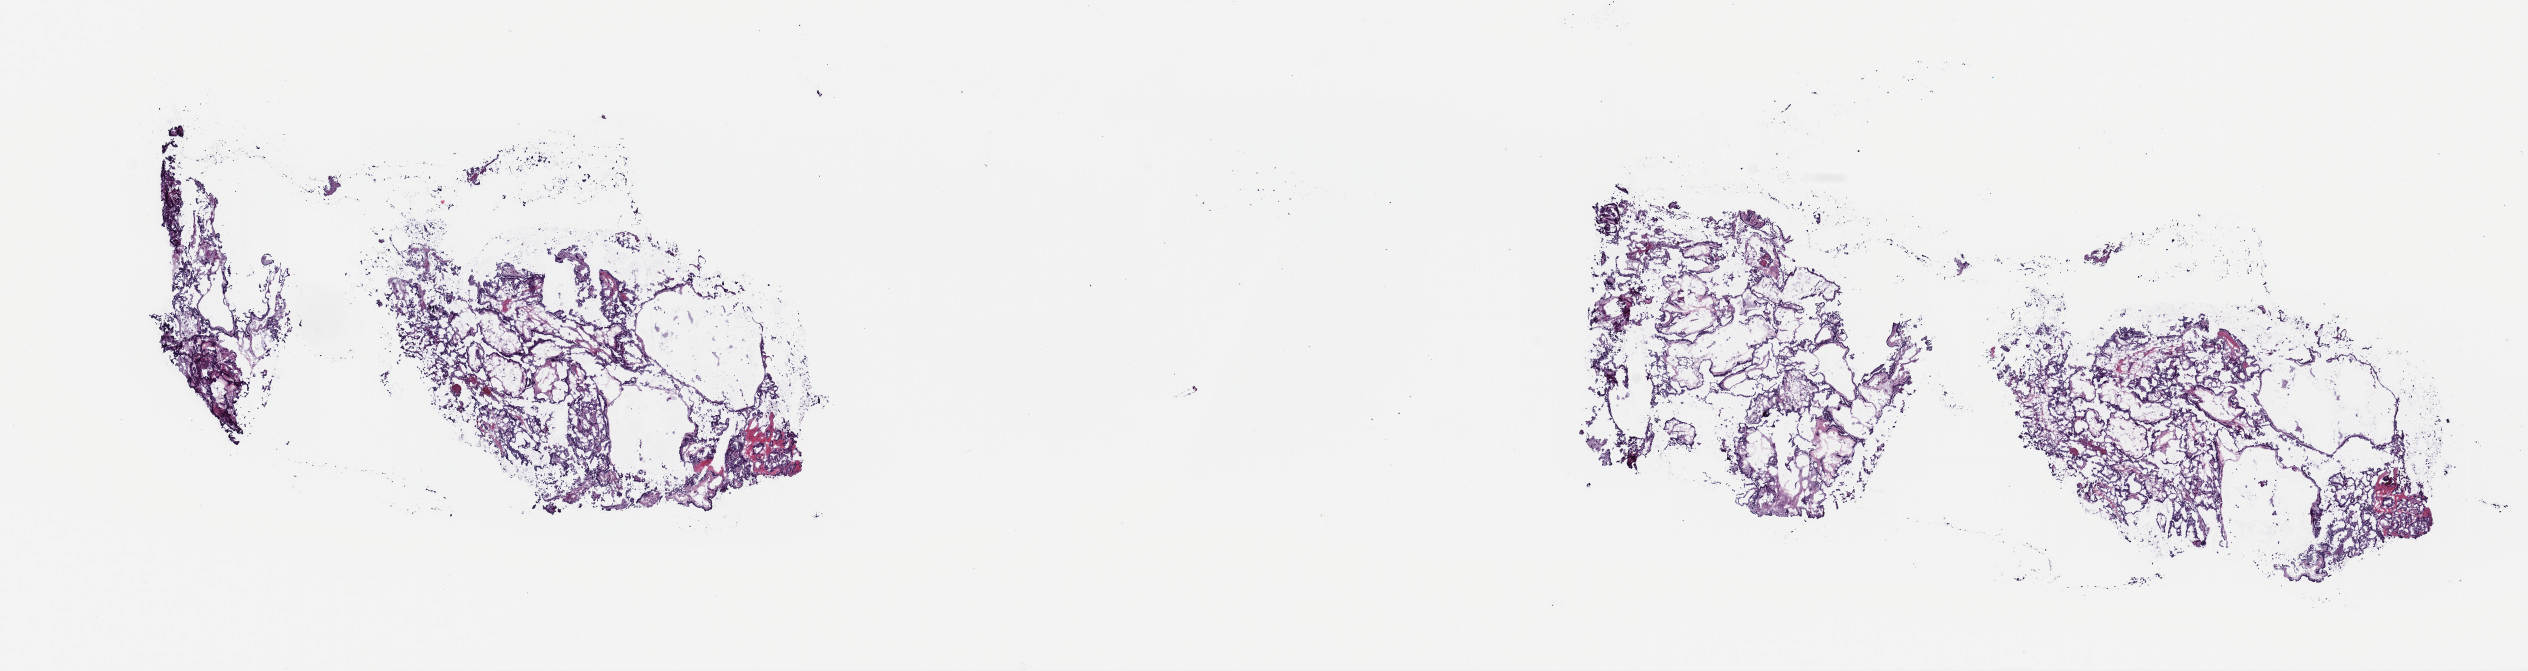
H&E whole-slide image, whole scanned area (about 20.0 x 5.3 mm, acquisition: 40x scan) shown as a low-resolution overview, frozen section, primary tumour sample from the thyroid. Female, age 40 years at initial diagnosis. Composition of this section per pathologist review: tumour cells 90%, tumour nuclei 90%, normal cells 0%, stromal cells 10%, necrosis 0%. Inflammatory infiltration, as recorded: lymphocyte infiltration 0%, monocyte infiltration 0%, neutrophil infiltration 0%.
Histologic diagnosis: Papillary adenocarcinoma, NOS (thyroid gland). AJCC pathologic stage: II. Laterality: right.